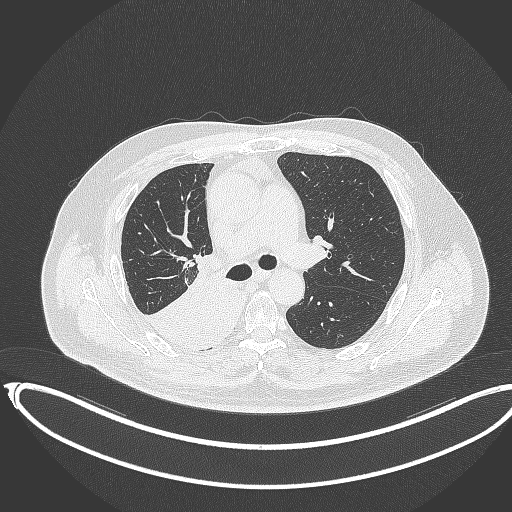
Chest CT, one axial slice; slice 226 of 403 in the series (ordered by position); reconstruction kernel B70f; 120 kVp; lung window (W 1500 / L -600 HU); 512 × 512 image matrix, field of view 436 × 436 mm. Patient: male, 68 years. From the clinical record (not read from this slice): clinical TNM (as recorded): T2a N0 M0.
Structures marked on this image (rectangle marked by the reading radiologist):
- lung tumour (recorded histology: adenocarcinoma): box from (x=147, y=257) to (x=228, y=347) px